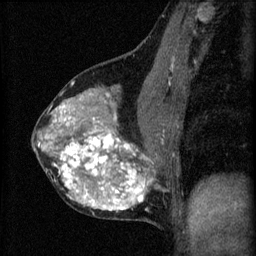
Breast MRI (dynamic contrast-enhanced), one sagittal slice; slice 32 of 60 in the series (ordered by position); 3 images stored at this slice position (order not interpretable as contrast timing); 1.5 T; TE 4.2 ms, TR 8.2 ms; 2 mm slice thickness; 256 × 256 image matrix. Patient: female, 40 years.
Outlined on this slice (semi-automatically segmented with operator editing):
- analysis volume of interest (the breast-tissue region the enhancement analysis was run in; not a lesion): bounding box <32,76,179,219> (left, top, right, bottom; pixels)
- tumour enhancement mask (voxels above the 70 % enhancement threshold inside the analysis volume of interest): <38,84,153,211>